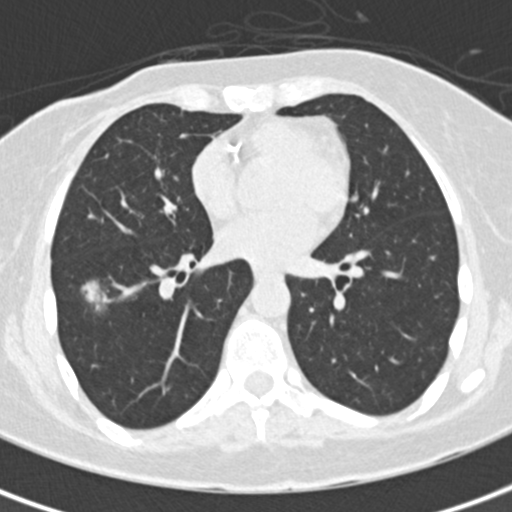
Low-dose screening chest CT, axial slice. Baseline annual screen. Lung window (W 1500 / L -600 HU). Slice 93 of 171 in the series. 512 × 512 image matrix, field of view 284 × 284 mm. Female participant, aged 56 years at enrolment. Former smoker at enrolment.
- Expert-annotated lung lesion, bounding box (x1, y1, x2, y2) in pixels: (73, 274, 131, 328).
- The screening reader recorded 5 non-calcified nodules or masses ≥4 mm on this exam (right lower lobe, right upper lobe, left upper lobe, left lower lobe, left lower lobe); which of them this box marks is not recorded.
- Lung cancer was diagnosed 26 days after this screen: bronchiolo-alveolar carcinoma, mucinous, right lower lobe, well differentiated (G1), stage IA (AJCC 6th edition), 19 mm at pathology.